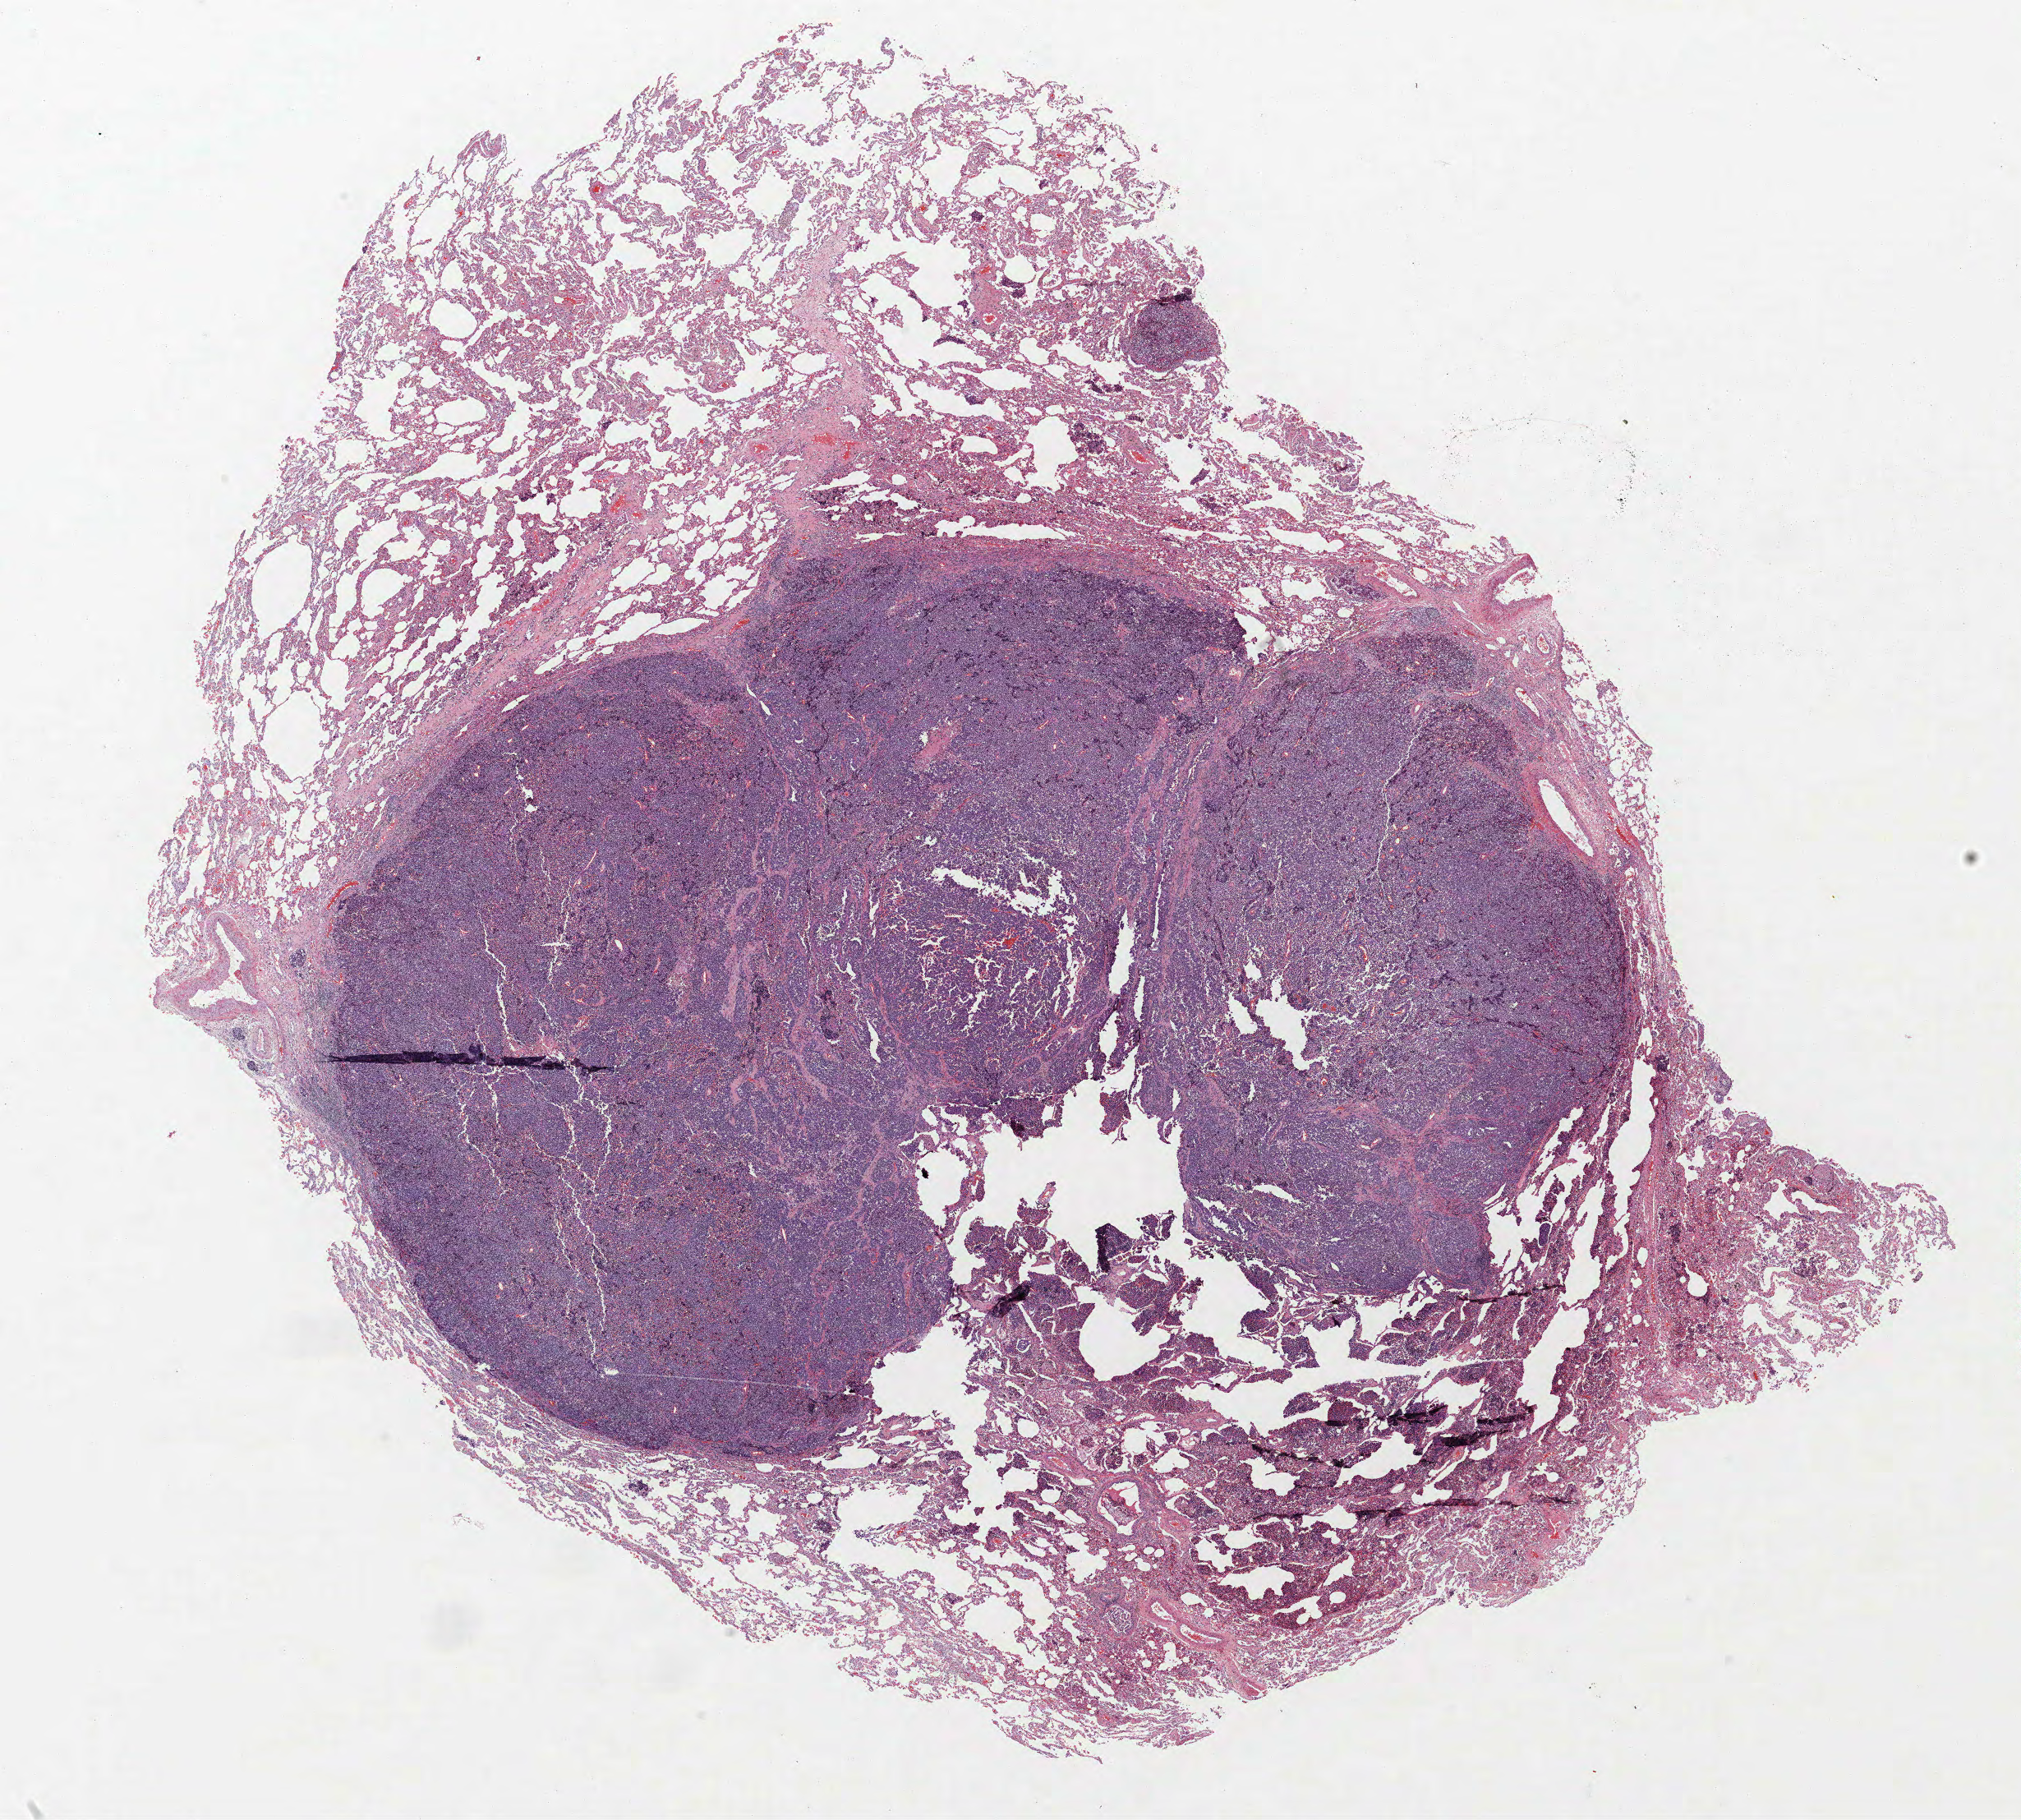
Whole-slide histology image, Hematoxylin and eosin (H&E) stained — whole scanned area (about 19.7 x 17.7 mm, acquisition: 40x scan) shown as a low-resolution overview, FFPE section, lung. Female patient, aged 64 at enrolment. Current smoker at enrolment.
Participant's lung-cancer diagnosis: Large cell neuroendocrine carcinoma.